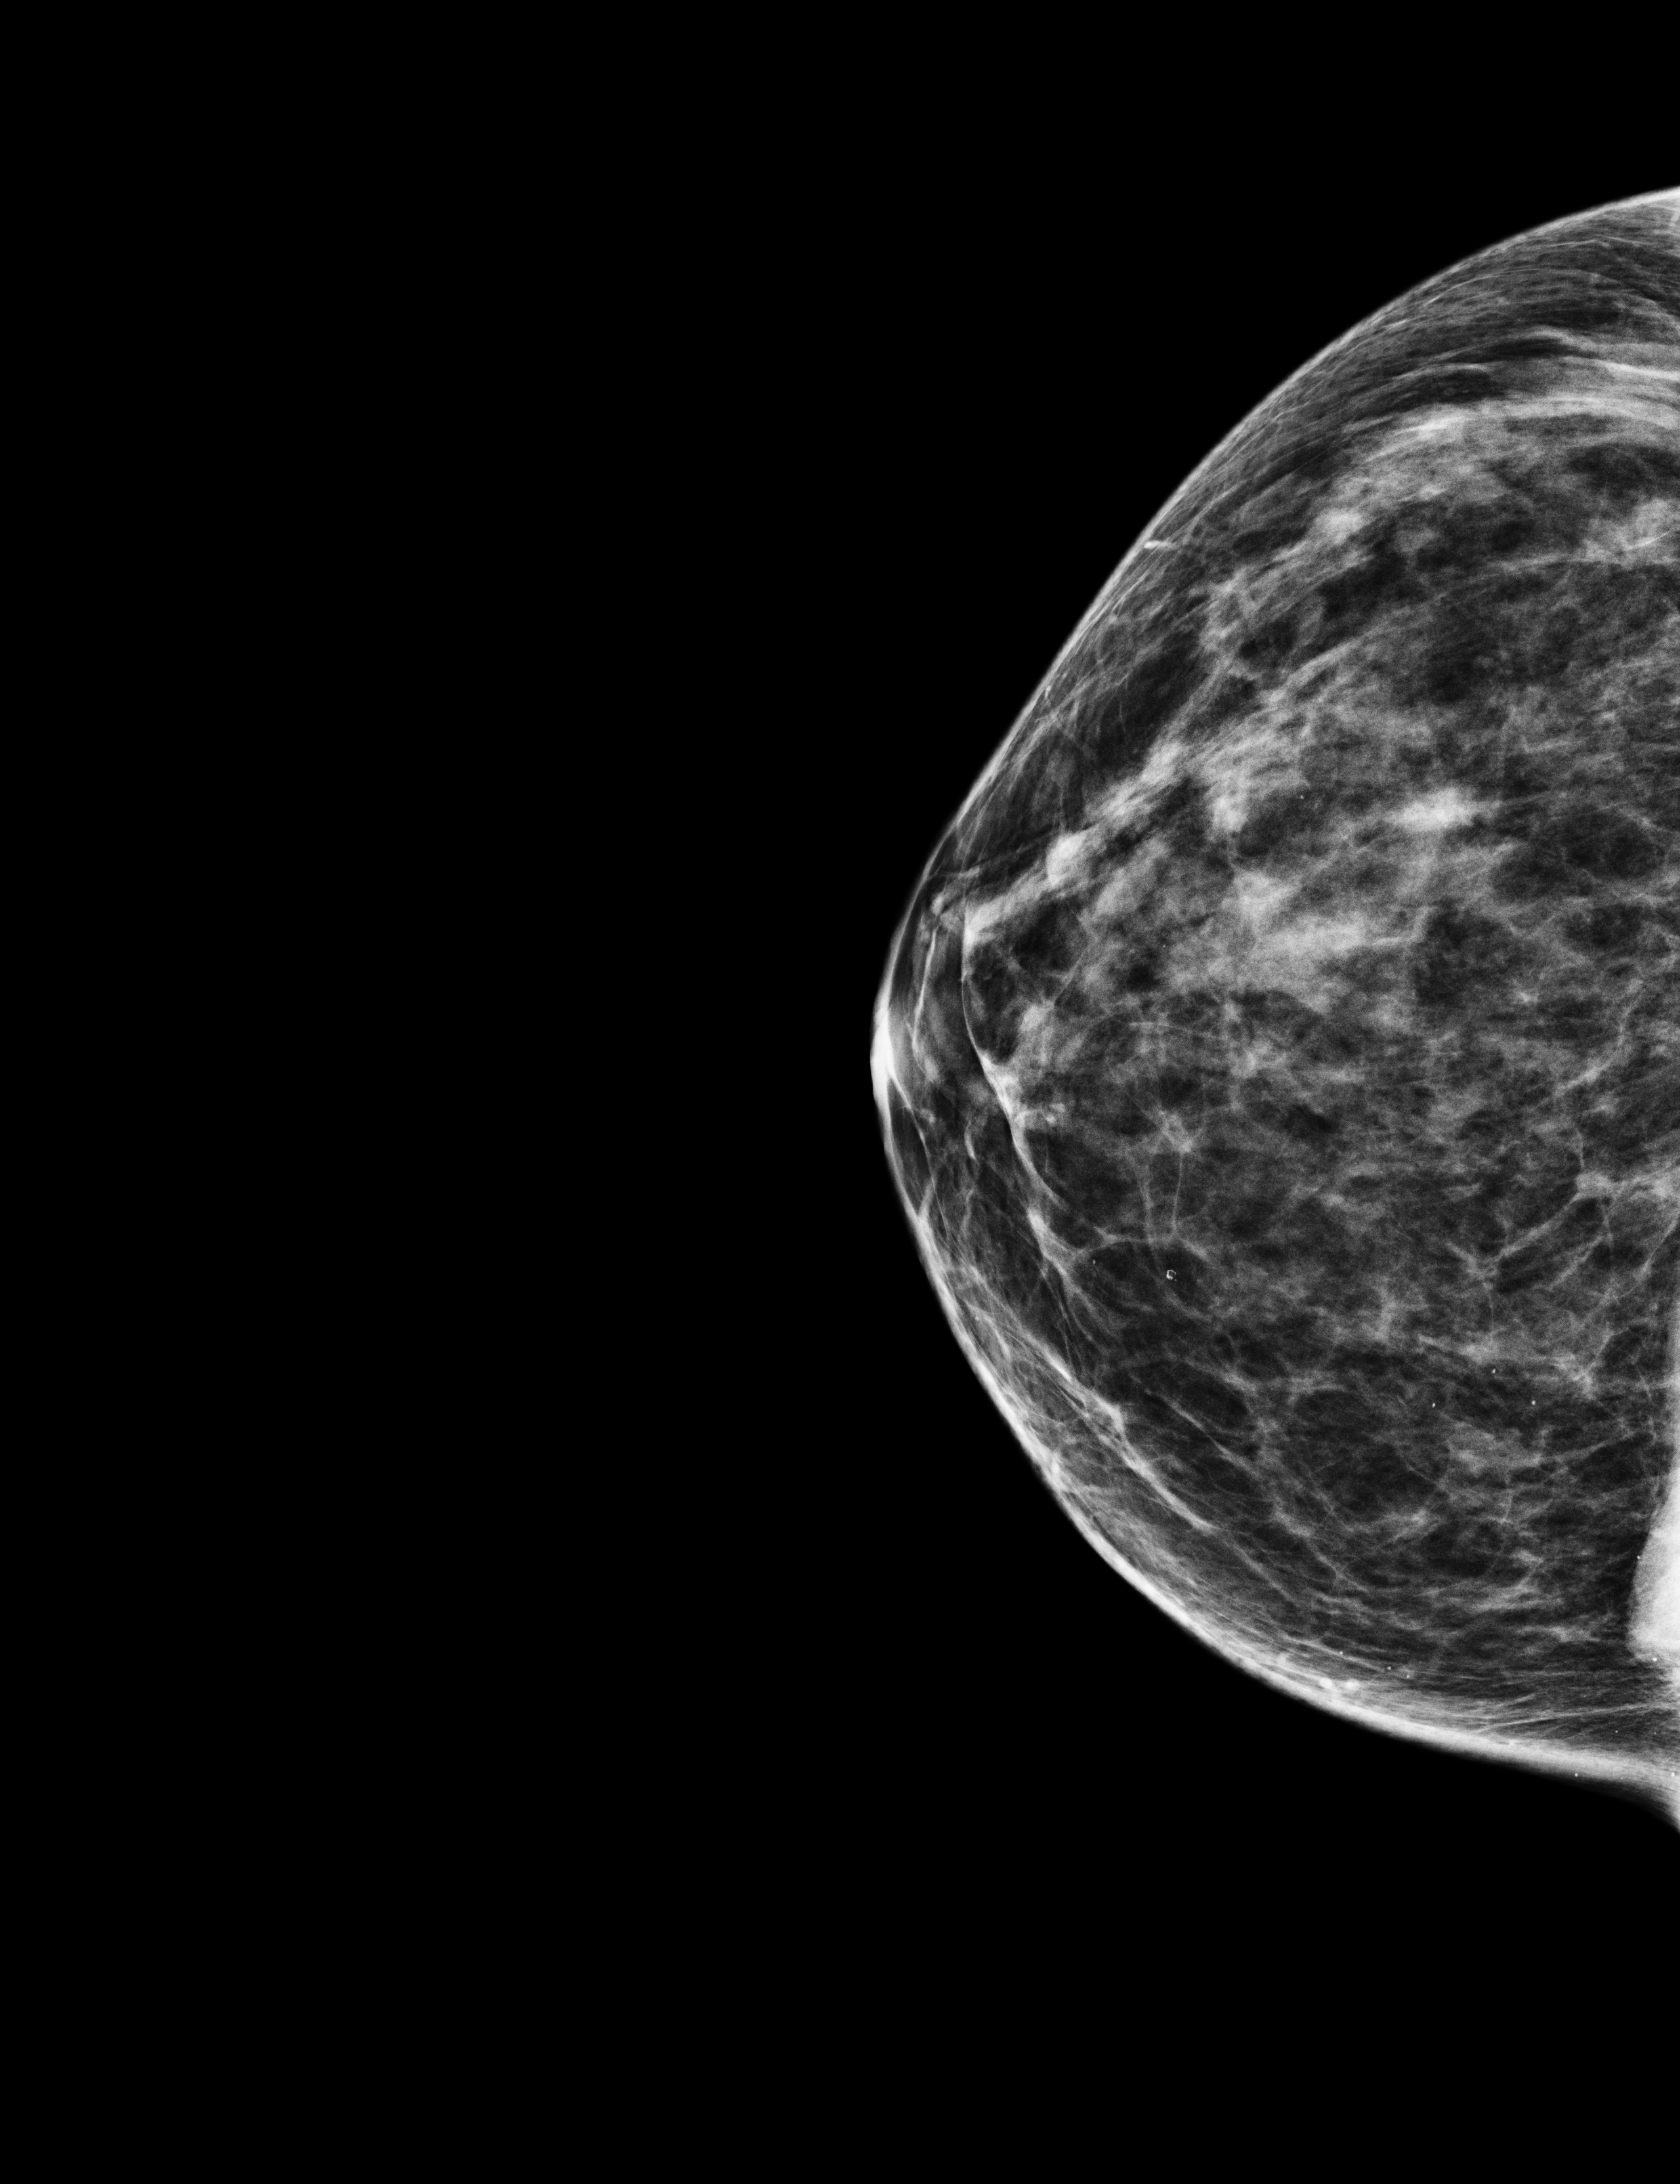
Annual screening mammography examination; compressed breast thickness 43 mm. Female patient, age 44 years.
Image type: full-field digital mammogram. Breast: right. Projection: CC view.